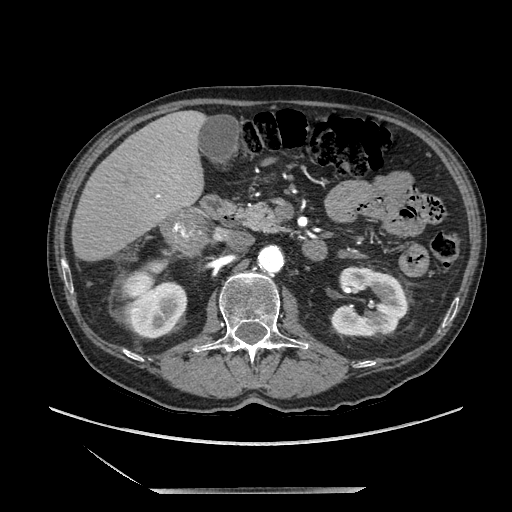
Contrast-enhanced abdominal CT, one axial slice. Slice 96 of 243 in the series (ordered by position). Soft-tissue window (W 400 / L 40 HU). 512 × 512 image matrix. Male patient. From the clinical record (not read from this slice): diagnosis: adrenocortical carcinoma; tumour side: right adrenal; tumour size at pathology: 16 cm; Ki-67 index: 17 %; stage (as recorded): 3.
Annotated regions visible in this slice (semi-automatic segmentation, software-assisted and operator-edited):
- mass: bounding box [x1, y1, x2, y2] px = [168, 211, 208, 251]